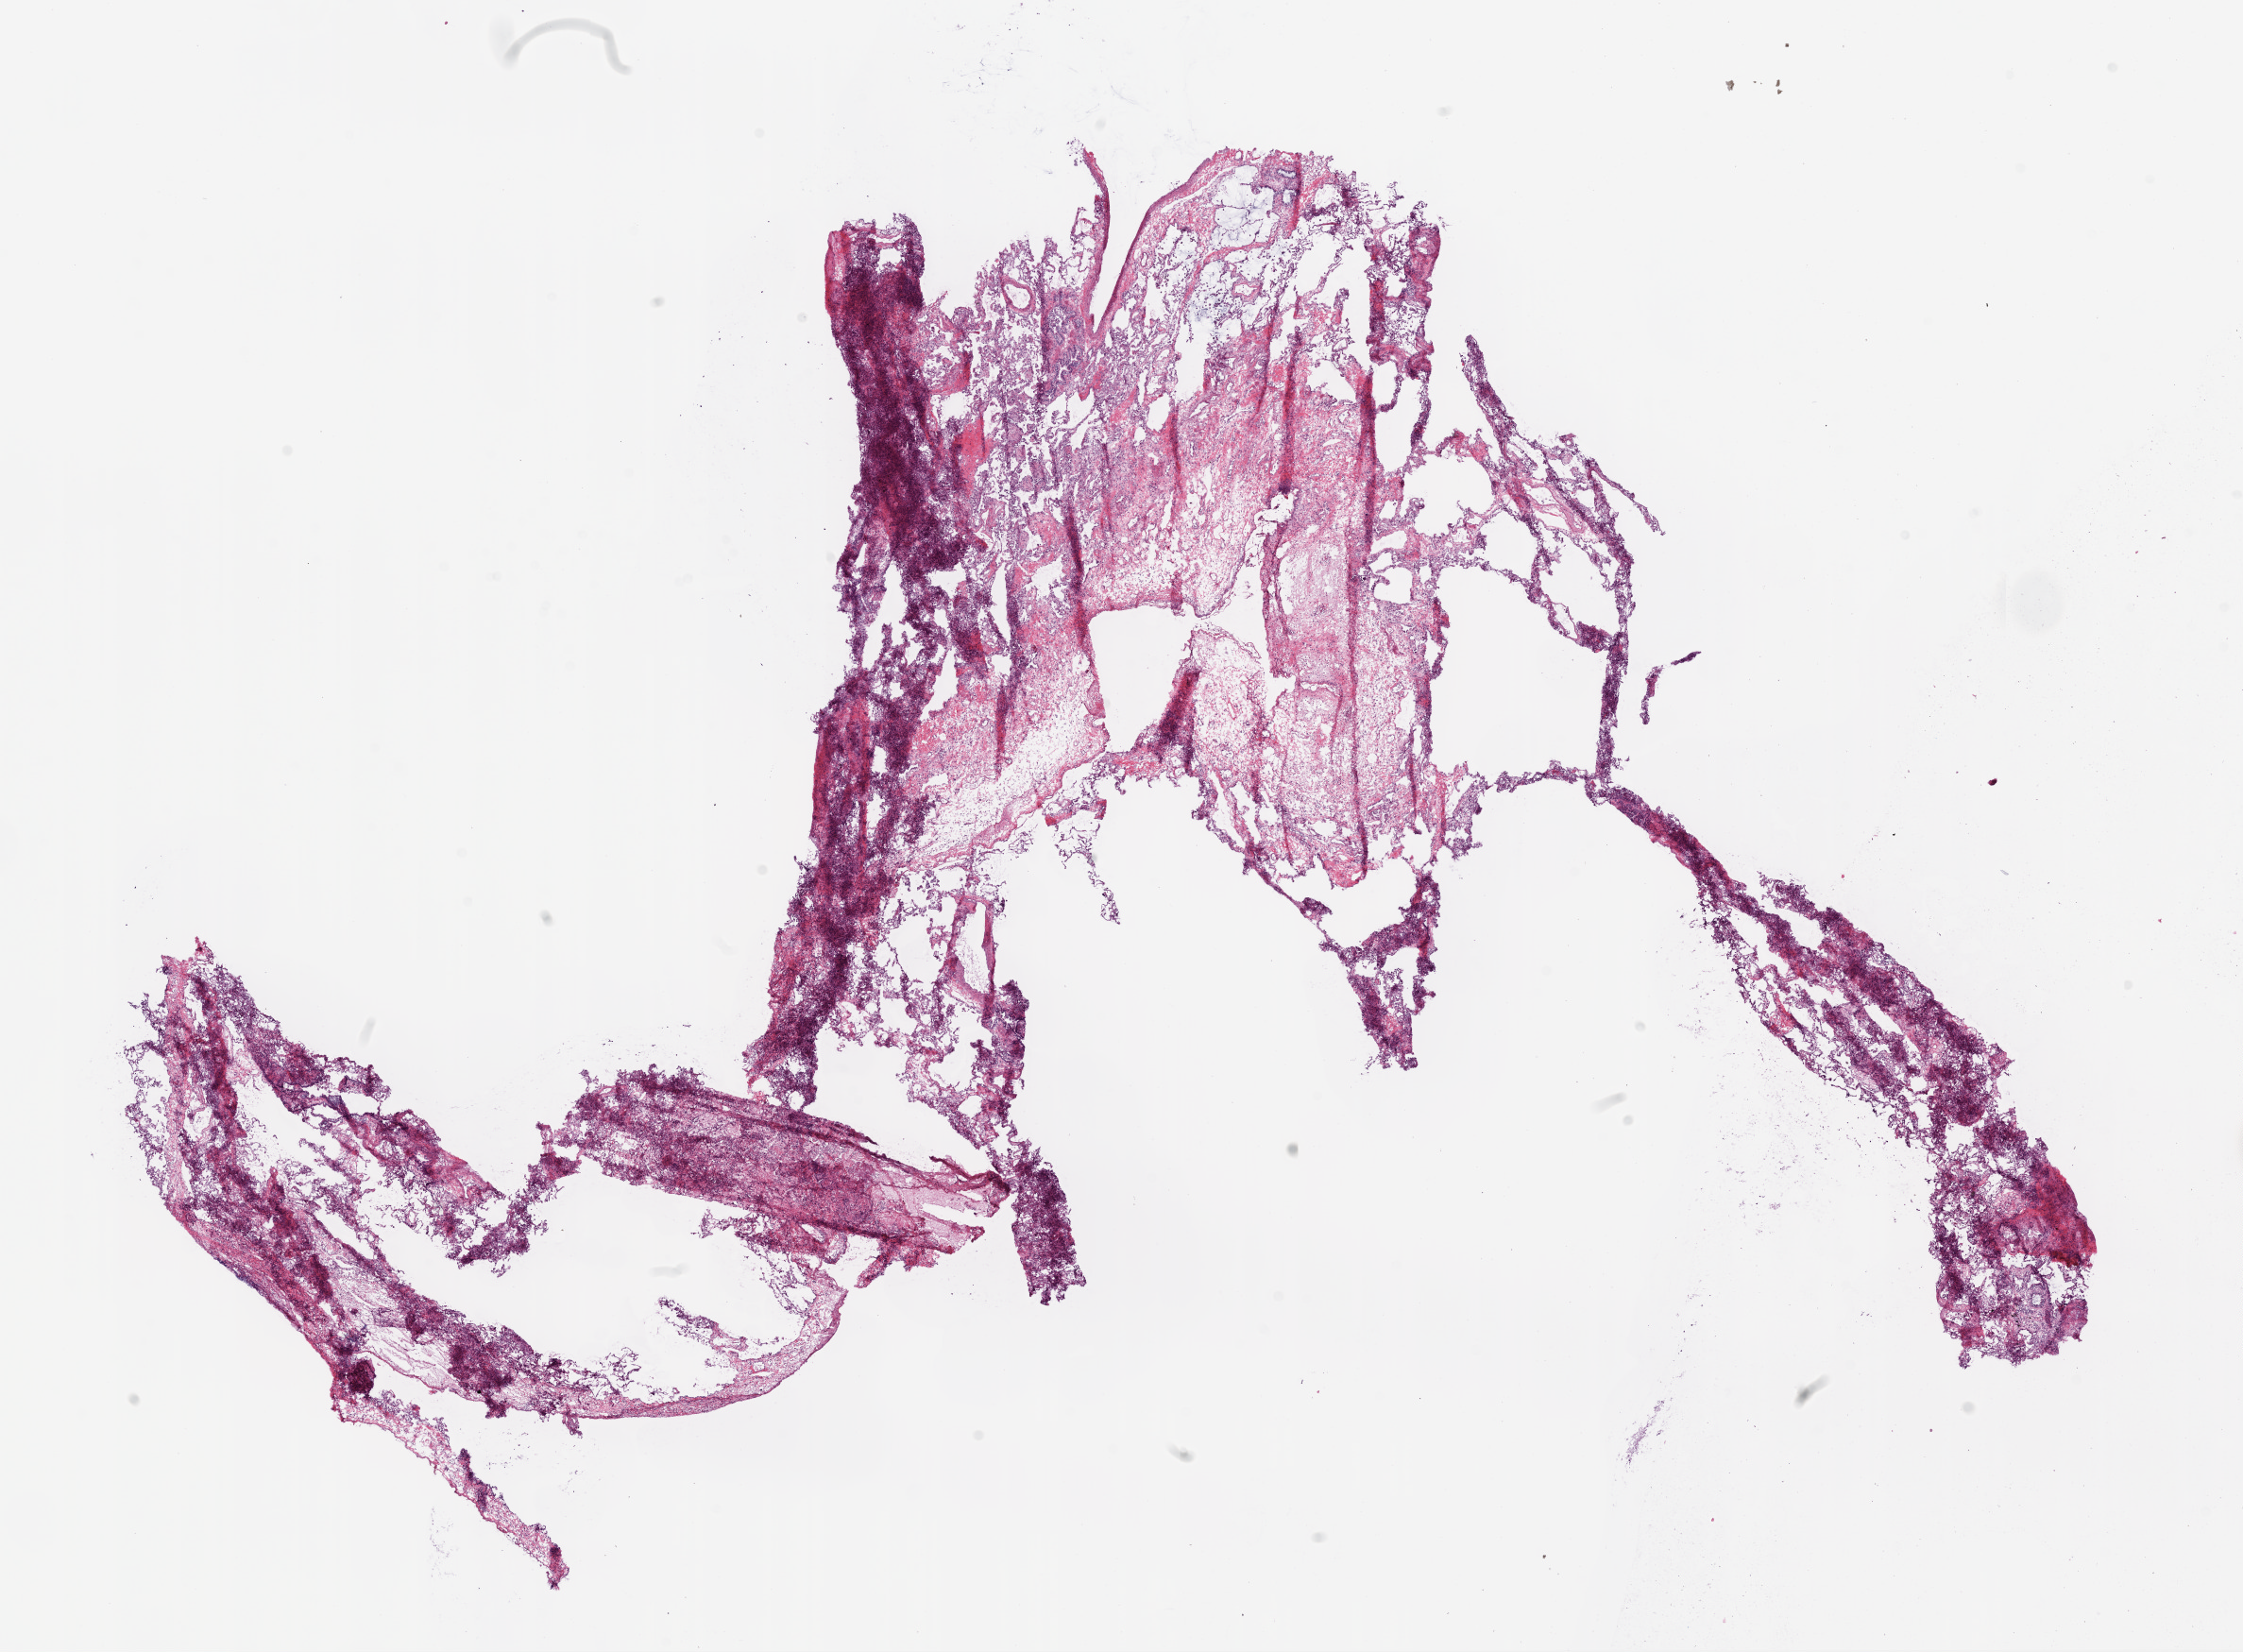
Whole-slide histology image, H&E-stained — a low-resolution overview of the entire scanned area, about 19.1 x 14.0 mm (from a 20x scan). Frozen section. Solid tissue normal (non-tumour tissue) sample from the lung. Patient: male, age at initial diagnosis 70 years.
• this section: solid tissue normal sample (biorepository sample class)
• patient diagnosis: Squamous cell carcinoma, NOS